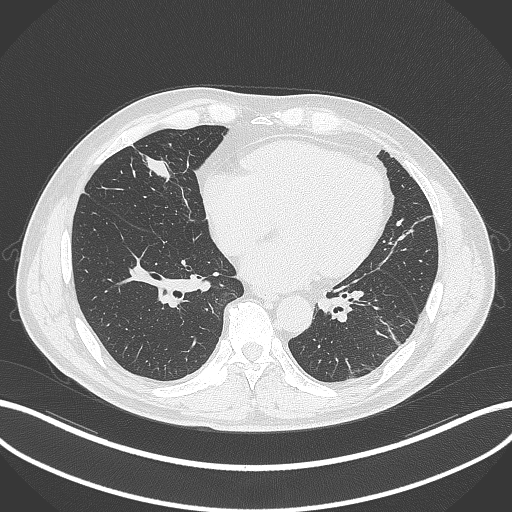
Chest CT, one axial slice. Position 100 of 399 along the scan axis. Reconstruction kernel B70f. 120 kVp. Lung window (W 1500 / L -600 HU). 1 mm slice thickness. 512 × 512 image matrix, field of view 400 × 400 mm. Male patient, age 59 years. Case-level facts recorded for this patient, not image findings: clinical TNM (as recorded): T2a N1 M0.
Structures marked on this image (bounding box drawn by a radiologist):
- lung tumour (recorded histology: adenocarcinoma): bounding box [x1, y1, x2, y2] px = [139, 150, 180, 189]